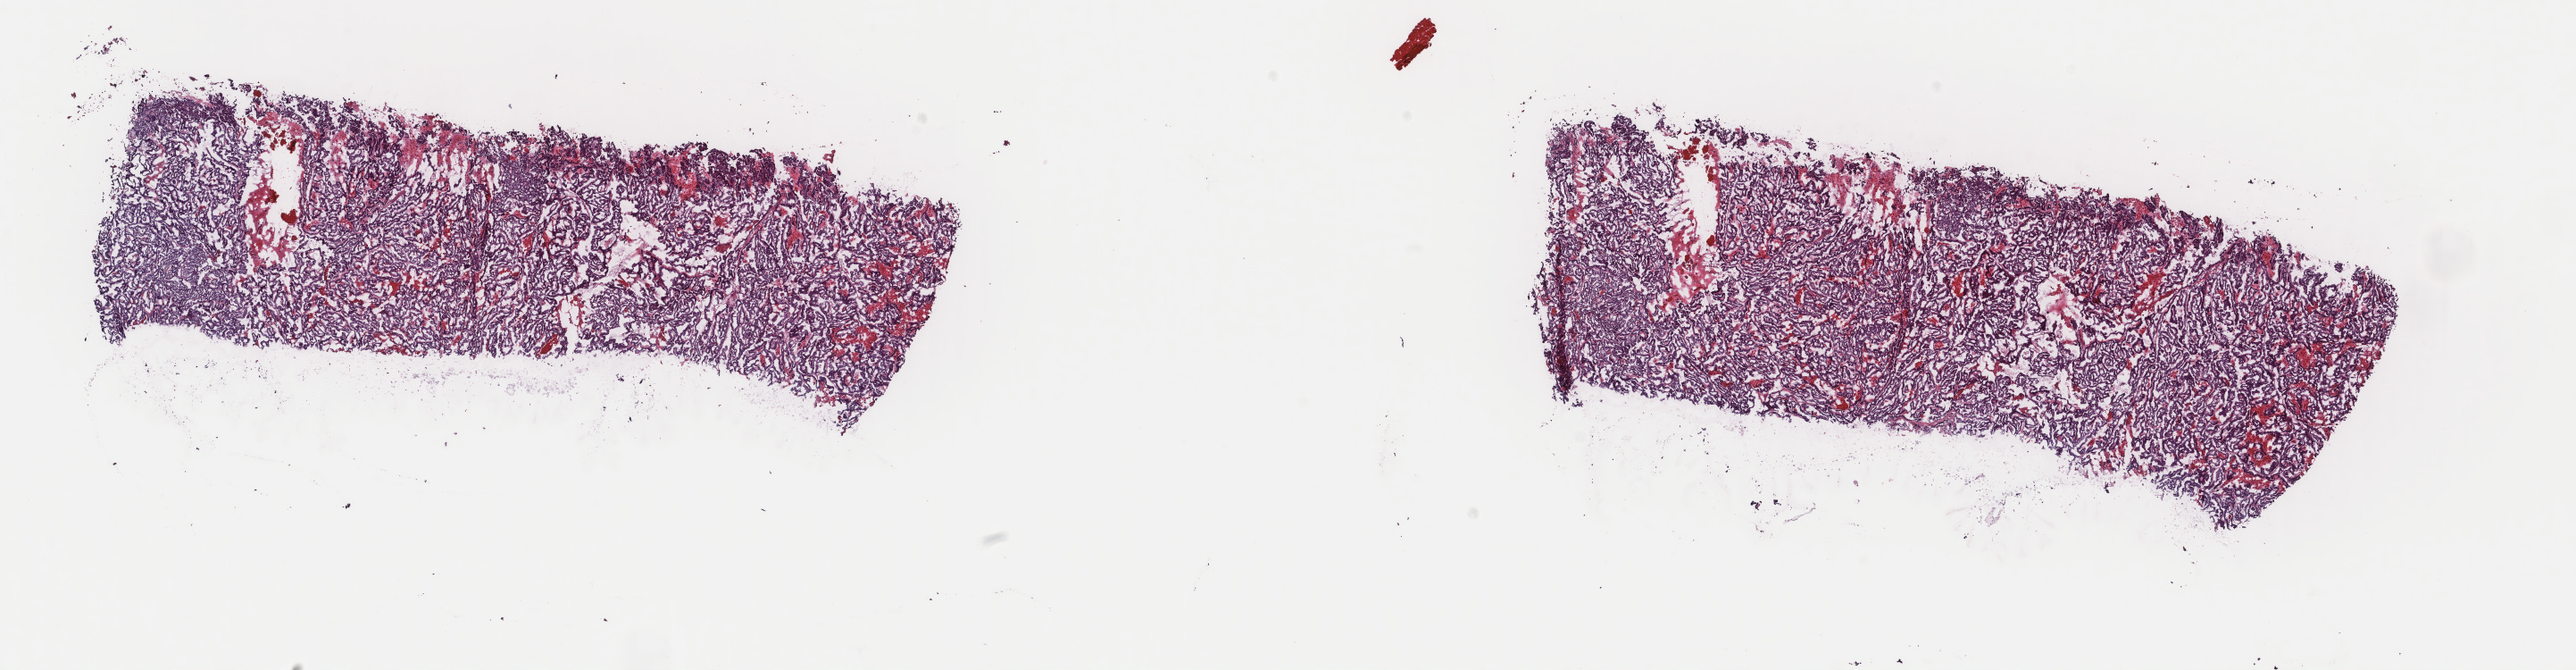
H&E whole-slide image — low-resolution overview of the scanned area, about 22.9 x 6.0 mm (from a 40x scan); frozen section; primary tumour sample from the thyroid. Patient: female, age at initial diagnosis 75 years. Slide review estimates, as recorded: tumour cells 90%, tumour nuclei 90%, normal cells 0%, stromal cells 10%, necrosis 0%. Infiltration values recorded for this section: lymphocyte infiltration 2%, monocyte infiltration 1%, neutrophil infiltration 1%.
- diagnosis: Papillary adenocarcinoma, NOS
- laterality: right
- AJCC pathologic stage: IVA